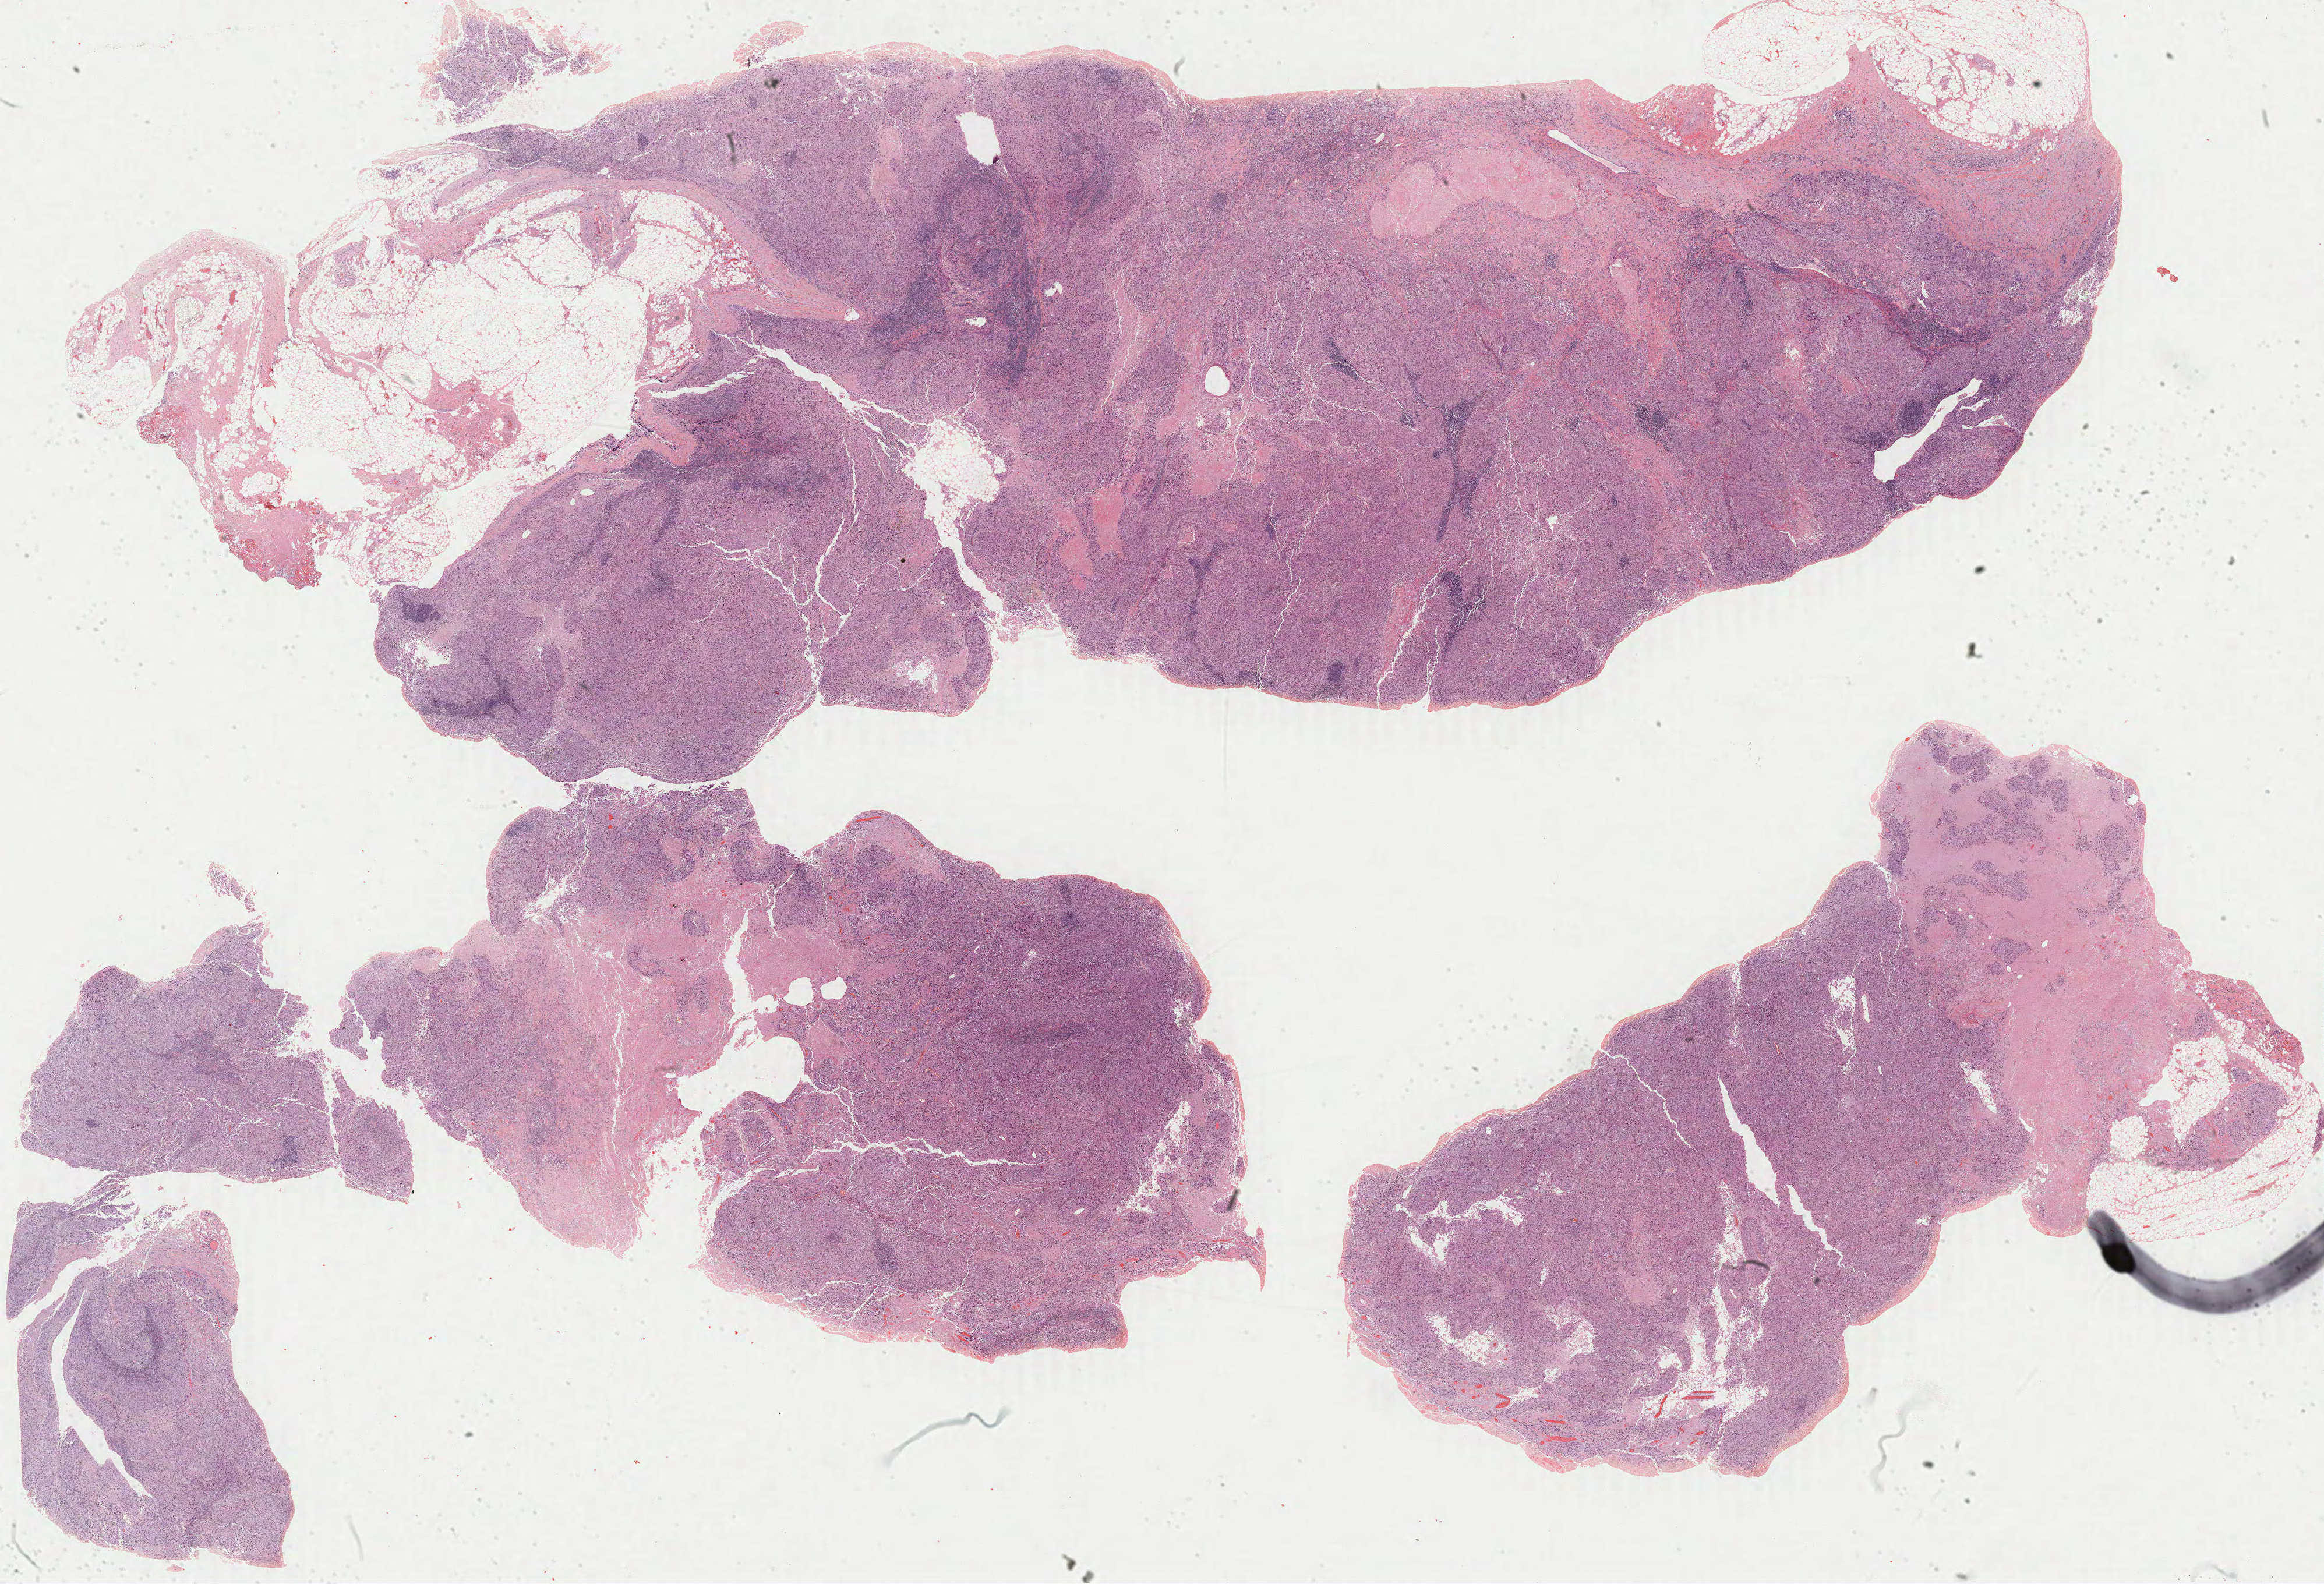
Whole-slide histology image, Hematoxylin and eosin (H&E) stained — low-resolution overview of the scanned area, about 32.0 x 21.8 mm (from a 40x scan), formalin-fixed paraffin-embedded (FFPE) diagnostic section, metastatic tumour sample, sampled site: lymph nodes of head, face and neck. Patient: male, age at initial diagnosis 73 years.
This section: metastatic tumour tissue. Patient diagnosis: Malignant melanoma, NOS.